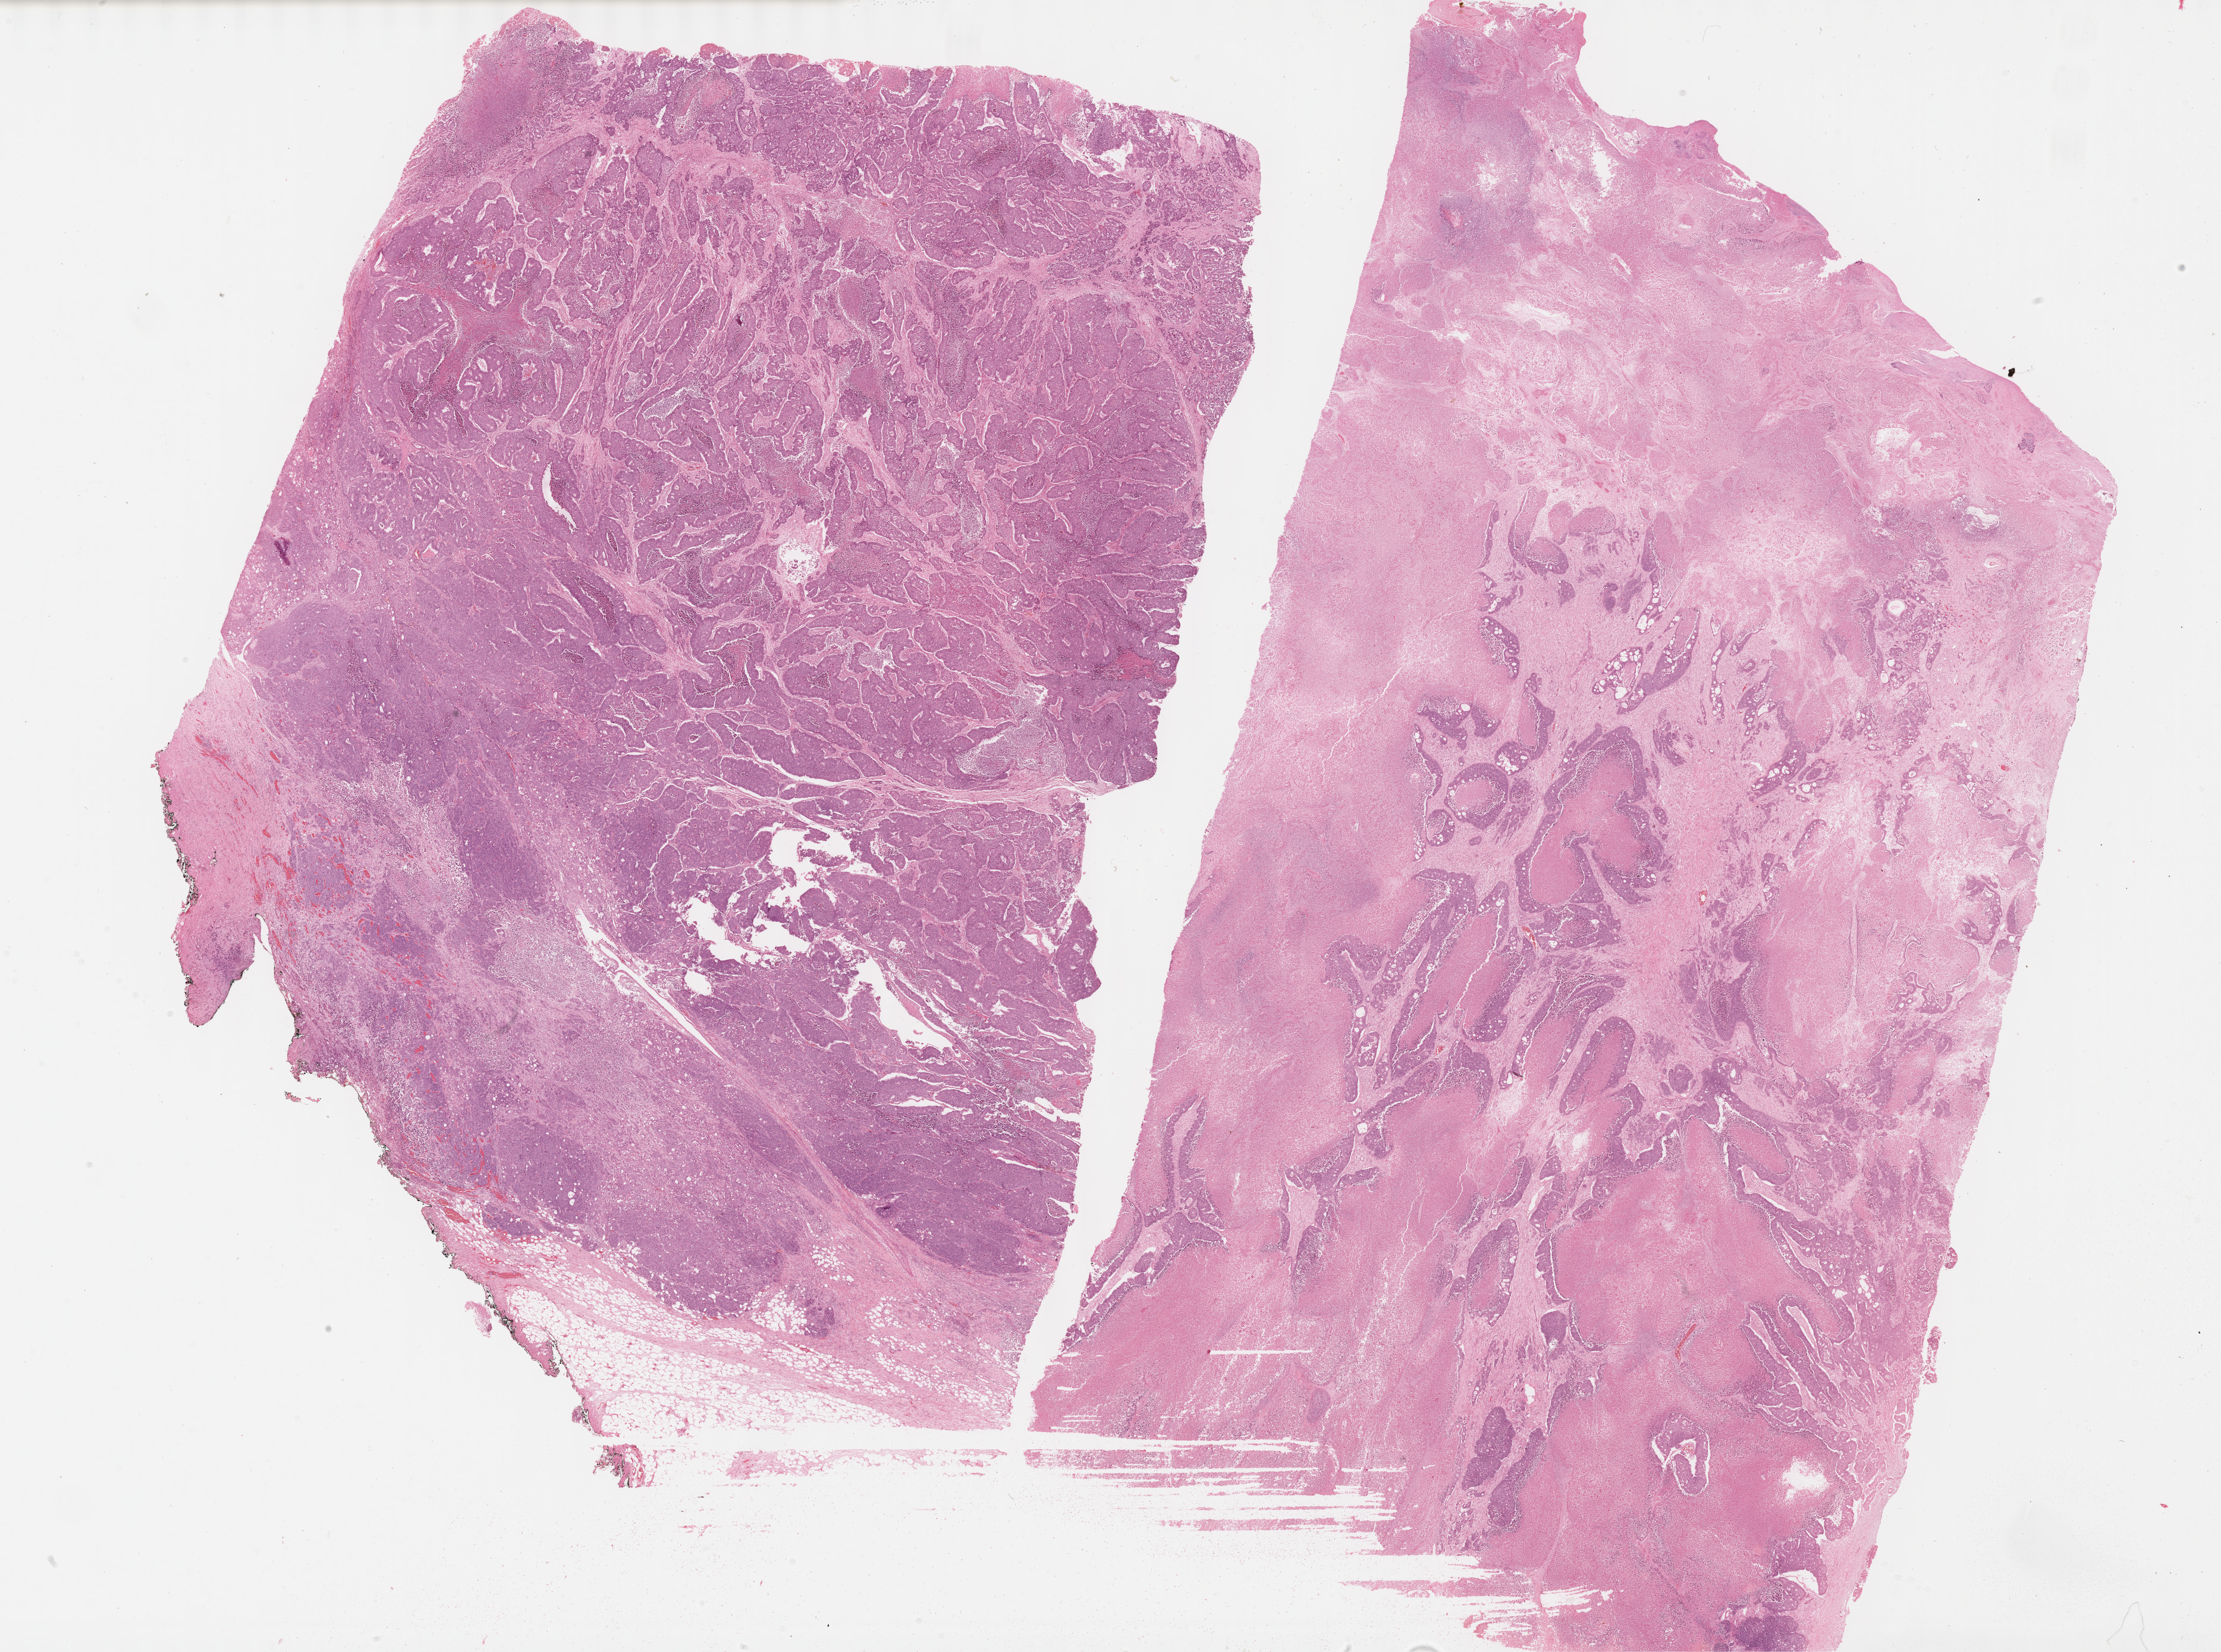
Digitized Hematoxylin and eosin (H&E) stained tissue section (whole slide), whole scanned area (about 30.2 x 22.4 mm, acquisition: 40x scan) shown as a low-resolution overview. Formalin-fixed paraffin-embedded (FFPE) diagnostic section. Primary tumour sample from the colon. Male patient; age at initial diagnosis 74 years.
- lymph nodes positive (case pathology): 0 of 3 examined
- diagnosis: Adenocarcinoma, NOS (ascending colon)
- TNM: T3 N0 M1b
- AJCC pathologic stage: IV (6th edition)